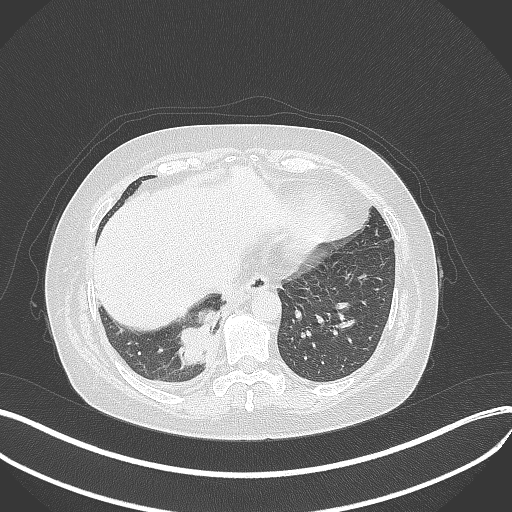
Chest CT, one axial slice; position 96 of 381 along the scan axis; reconstruction kernel B70f; 120 kVp; lung window (W 1500 / L -600 HU); 1 mm slice thickness; 512 × 512 image matrix. Female patient, age 56 years. Case-level facts recorded for this patient, not image findings: clinical TNM (as recorded): T2b N1 M0; histopathological grade: G3.
Structures marked on this image (rectangle marked by the reading radiologist):
- lung tumour (recorded histology: small cell carcinoma): bounding box <174,304,219,375> (left, top, right, bottom; pixels)